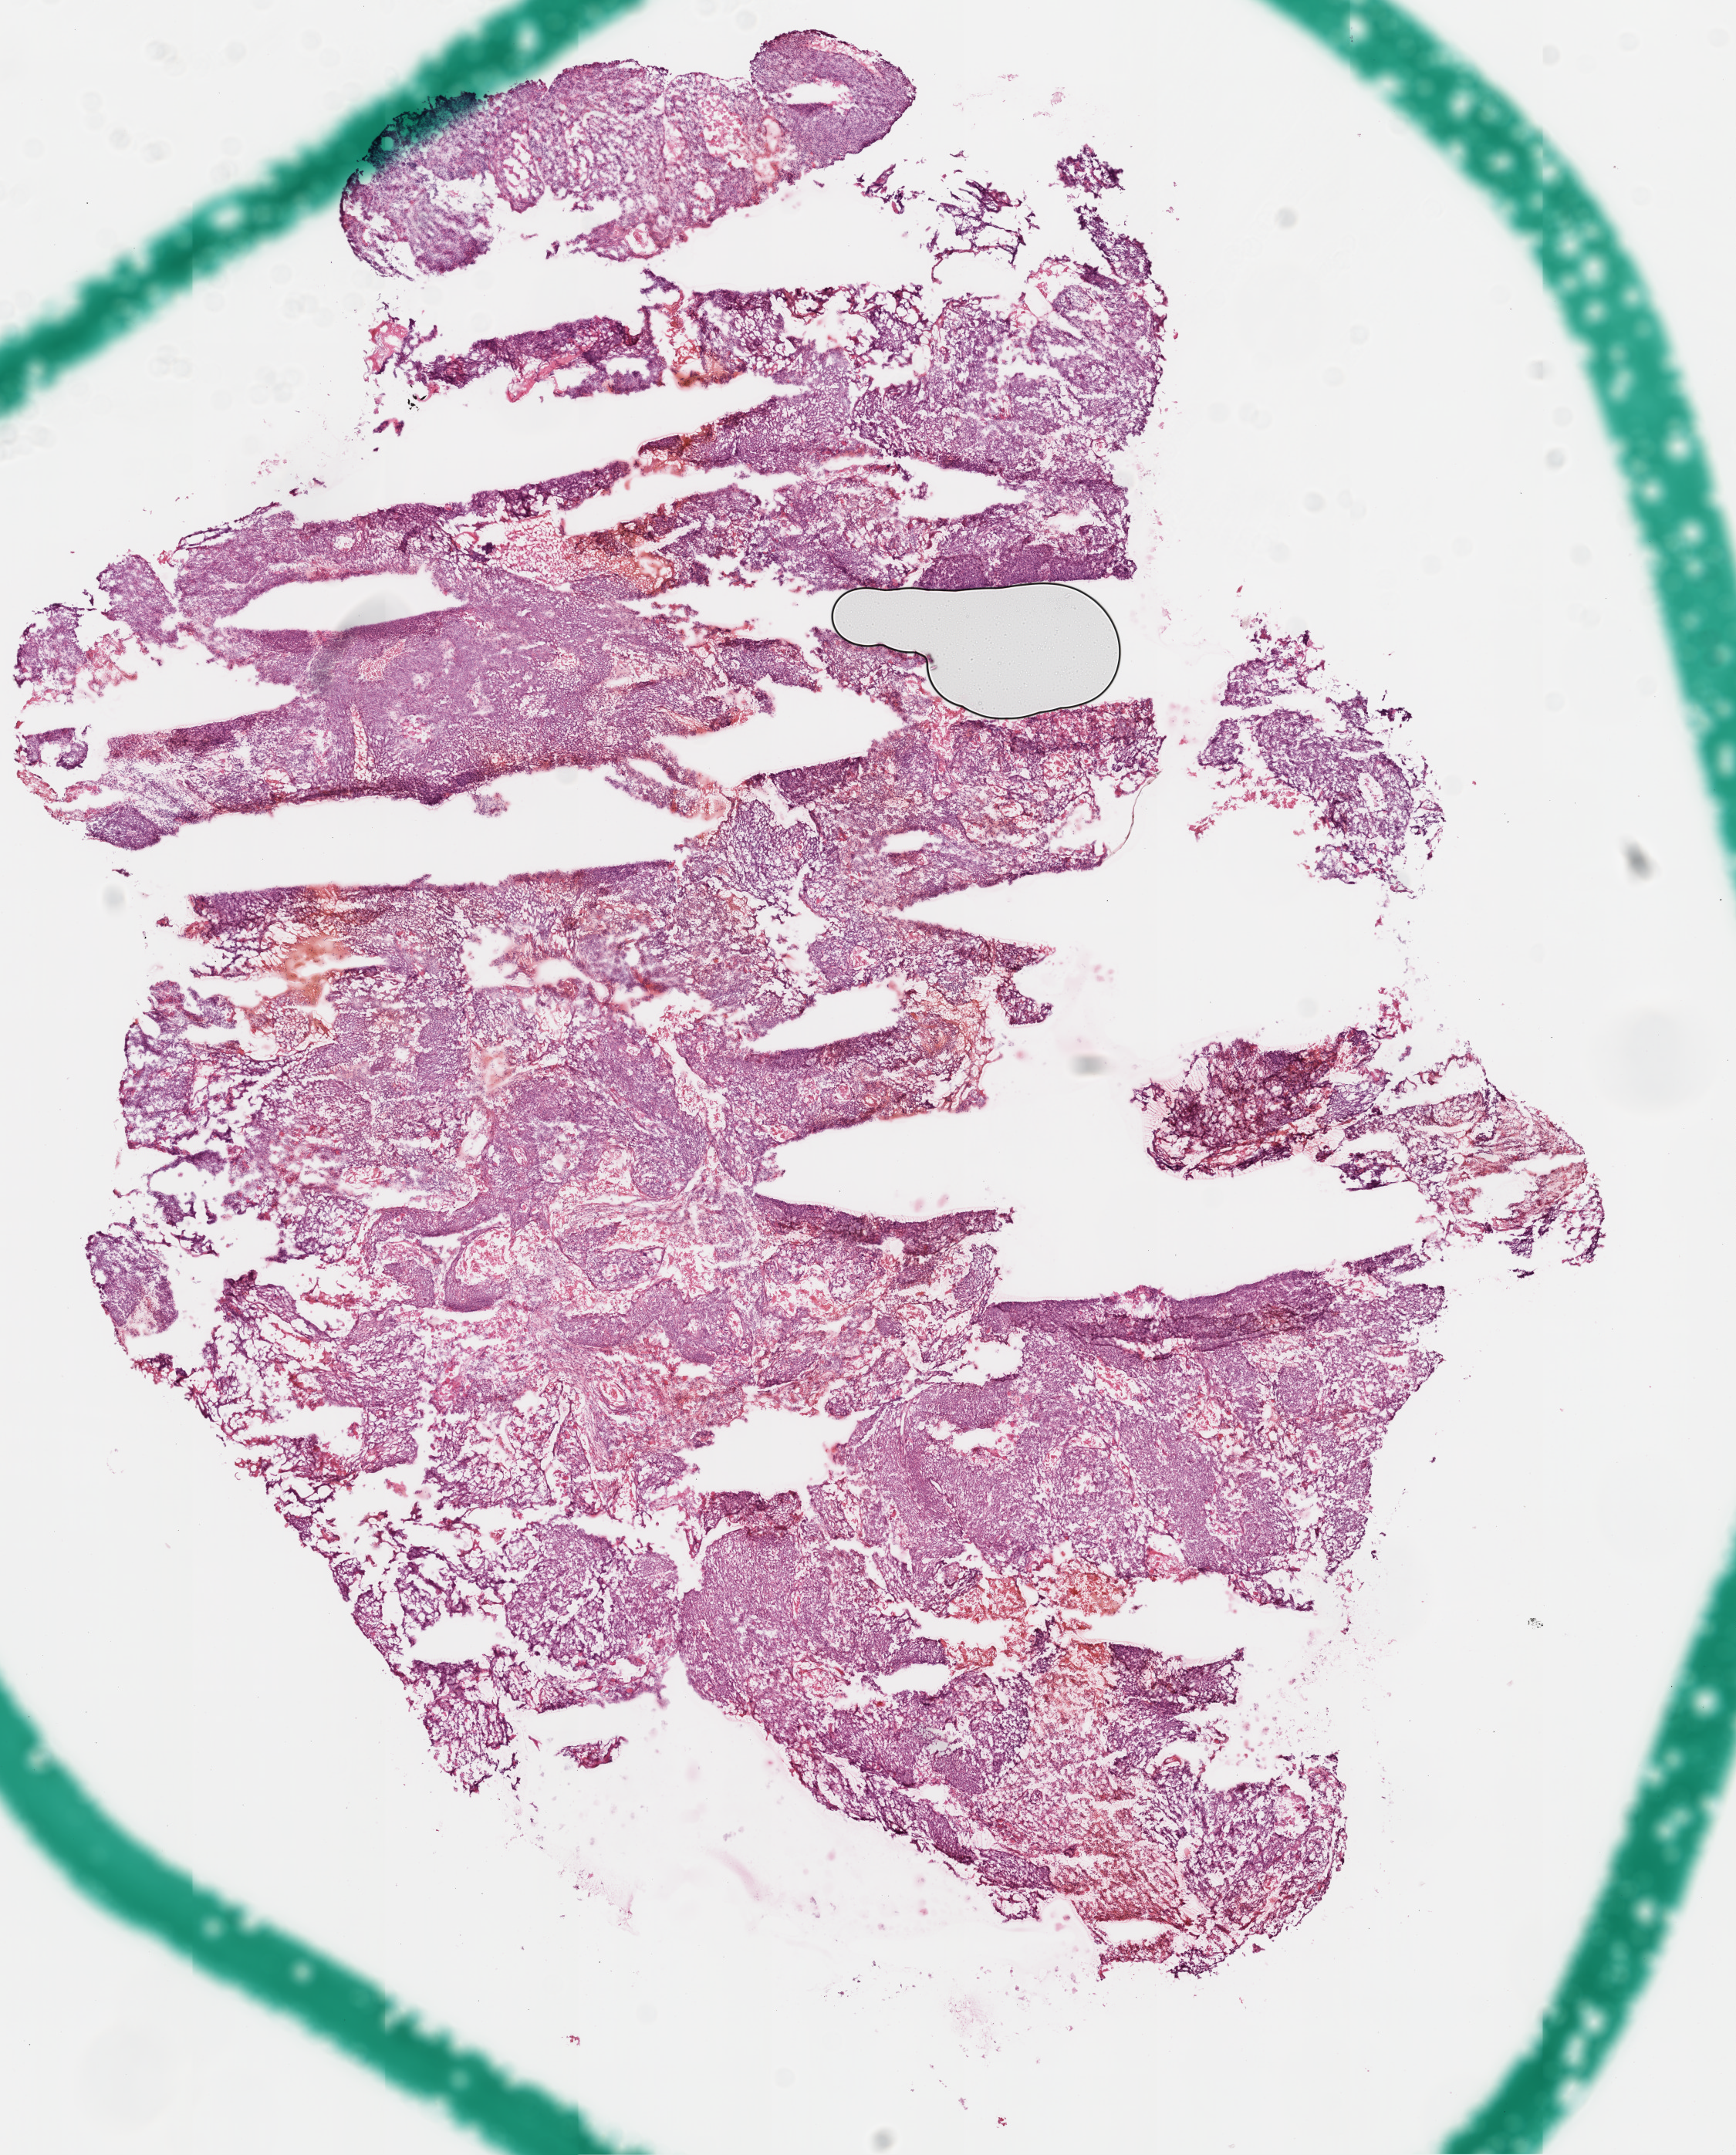
Whole-slide histology image, H&E, shown as a low-resolution overview of the whole scanned area (about 9.0 x 11.2 mm, from a 20x scan), frozen section from the top of the tissue portion, head and neck, primary tumour sample. Male, age 73 years at initial diagnosis. Histologic grade: G3 (poorly differentiated). Pathologist review of this section (percent, as recorded): tumour cells 81%, tumour nuclei 95%, normal cells 0%, stromal cells 0%, necrosis 19%. Inflammatory infiltration, as recorded: lymphocyte infiltration 1%.
Pathologic diagnosis: Squamous cell carcinoma, NOS (base of tongue, NOS).